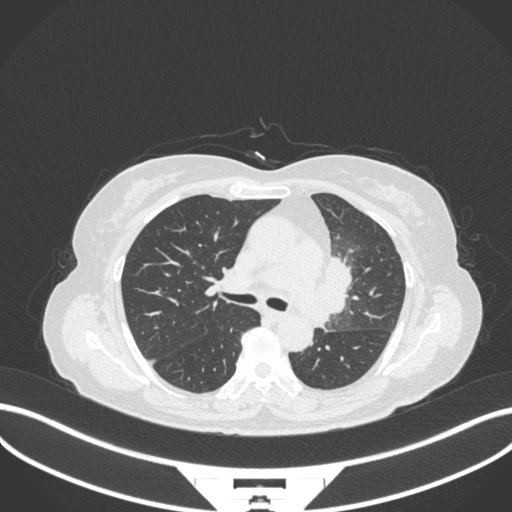
Chest CT, one axial slice. Slice 209 of 382 in the series (ordered by position). 120 kVp. Lung window (W 1500 / L -600 HU). 1 mm slice thickness. 512 × 512 image matrix. Female patient, age 64 years. From the clinical record (not read from this slice): clinical TNM (as recorded): T2a N2 M0.
Outlined on this slice (rectangle marked by the reading radiologist):
- lung tumour (recorded histology: adenocarcinoma): bounding box (x1, y1, x2, y2) in pixels: (313, 252, 356, 331)